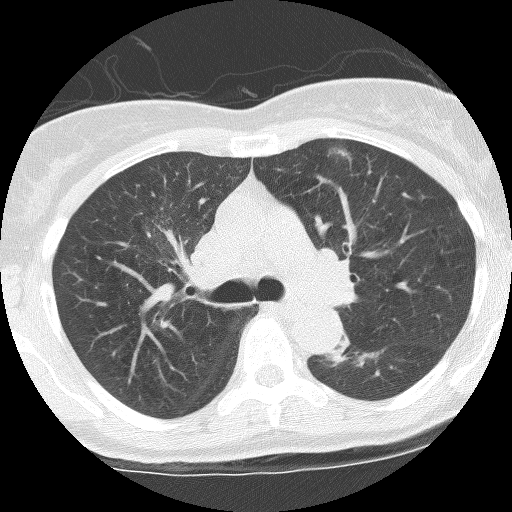
Chest CT (low-dose screening protocol), one axial image, third screening round (two years after baseline), lung window (W 1500 / L -600 HU), 2.5 mm slice thickness, lung (sharp) reconstruction kernel (BONE), slice 44 of 115 in the series. Female, age 62 years at enrolment.
- Expert-annotated lung lesion, bounding box [x1, y1, x2, y2] px = [320, 333, 392, 374].
- The screening reader recorded 3 non-calcified nodules or masses ≥4 mm on this exam; which of them this box marks is not recorded.
- Official screen result: positive, other.
- Later outcome: lung cancer diagnosed 165 days after this screen — squamous cell carcinoma, NOS, left lower lobe, stage IIIB (AJCC 6th edition), 31 mm at pathology.